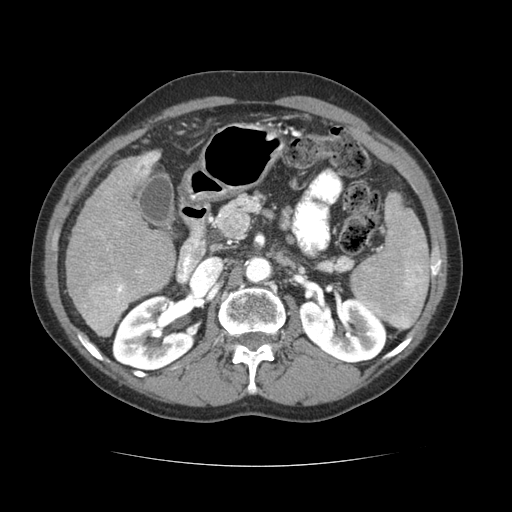
Contrast-enhanced abdominal CT (liver protocol), one axial slice. Slice 33 of 69 in the series (ordered by position). Reconstruction kernel STANDARD. Soft-tissue window (W 400 / L 40 HU). 512 × 512 image matrix, field of view 360 × 360 mm. From the clinical record (not read from this slice): diagnosis: hepatocellular carcinoma (patient treated with transarterial chemoembolisation; whether this scan precedes or follows treatment is not stated here); TNM stage (as recorded): Stage-II; Child-Pugh class: B; tumour differentiation: poorly differentiated; tumour size: 2.6 cm.
Structures marked on this image (semi-automatic segmentation, software-assisted and operator-edited):
- liver parenchyma outside the tumour (the mass and vessels are separate outlines, so this box may not span the whole liver): bounding box <66,150,174,336> (left, top, right, bottom; pixels)
- mass: <80,277,137,335>
- liver vessels: <133,153,159,273>